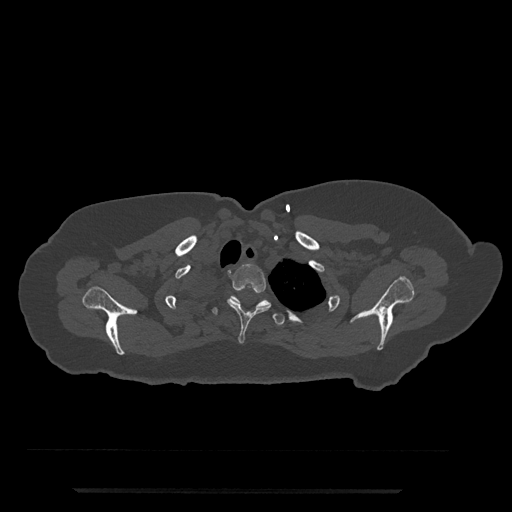
CT including the spine, one axial slice. Slice 663 of 797 in the series (ordered by position). Bone window (W 1800 / L 400 HU). 512 × 512 image matrix, field of view 440 × 440 mm. Patient: female, 51 years. Case-level facts recorded for this patient, not image findings: primary cancer: neuro; vertebrae with lytic lesions (as recorded): T8.
Annotated regions visible in this slice (semi-automatic segmentation, software-assisted and operator-edited):
- T2 vertebra: bounding box [x1, y1, x2, y2] px = [227, 264, 271, 344]
- T3 vertebra: [212, 295, 285, 326]